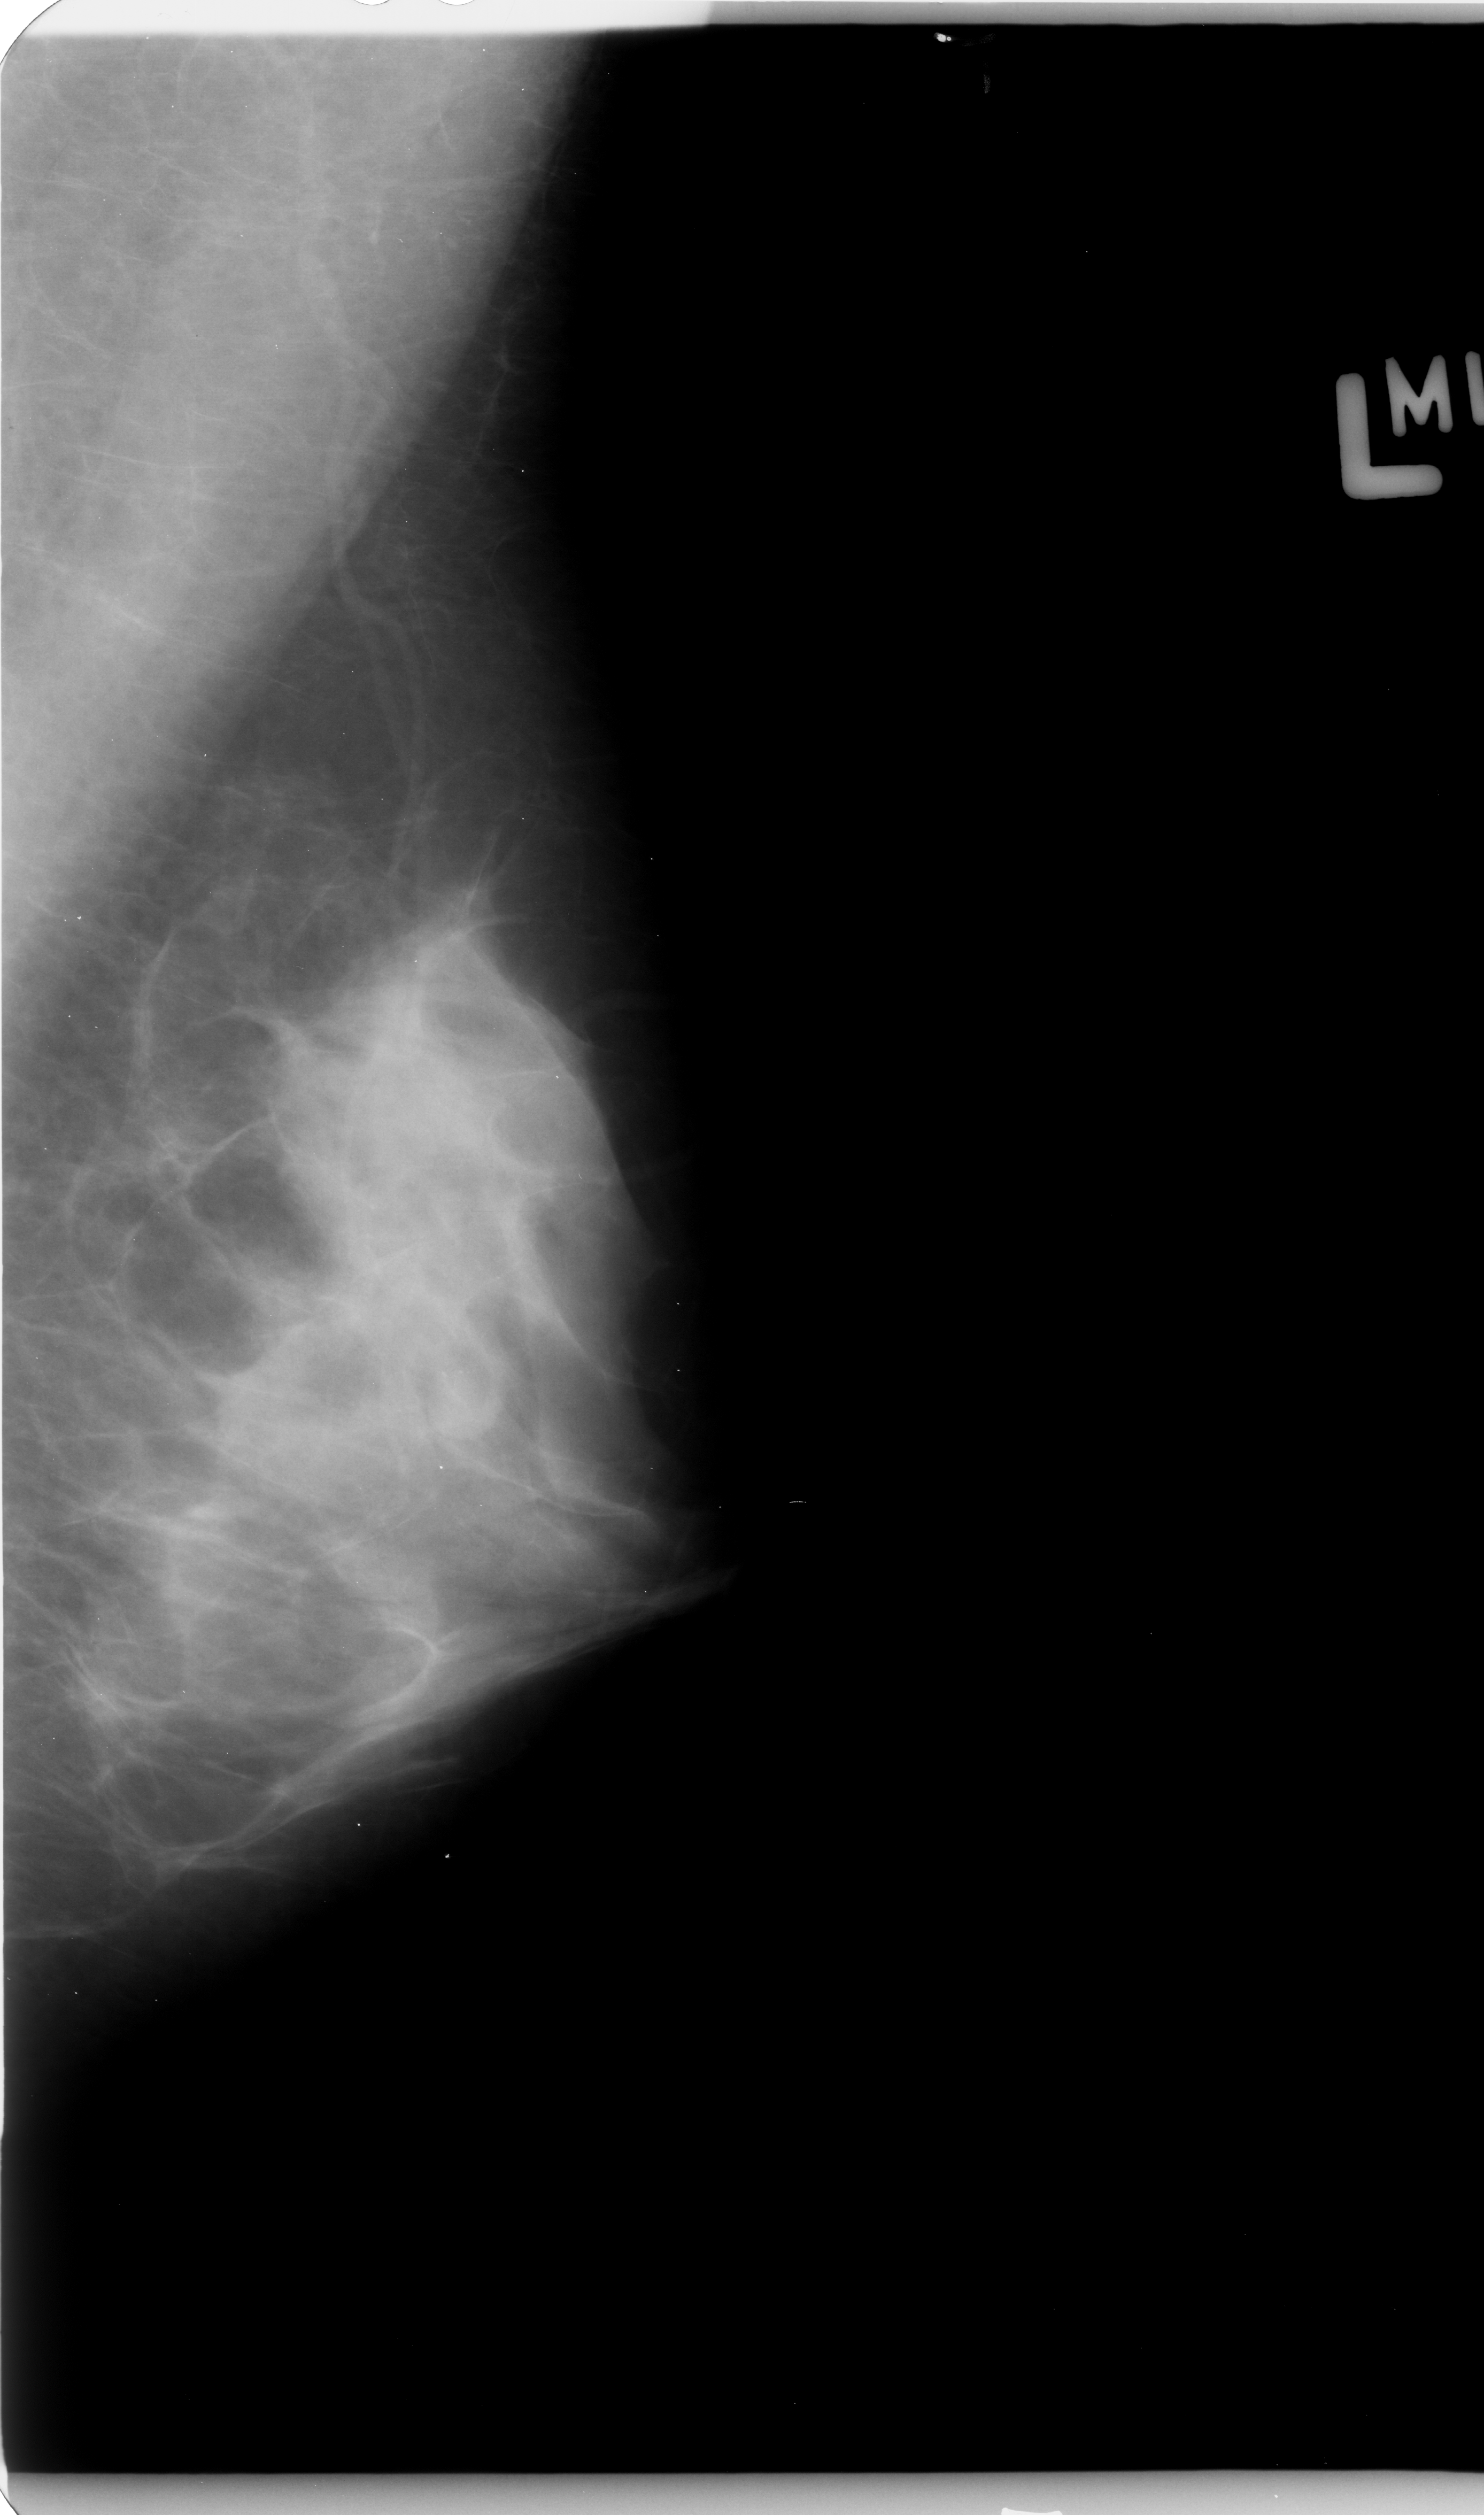
Scanned film-screen mammogram, left breast, mediolateral oblique (MLO) view, breast composition: extremely dense (BI-RADS density category 4 of 4).
Marked abnormality: mass, shape round, margins circumscribed; BI-RADS assessment category 3; subtlety rating 3 on a 1 (subtle) to 5 (obvious) scale; pathology result (as recorded, not read from the image): benign.